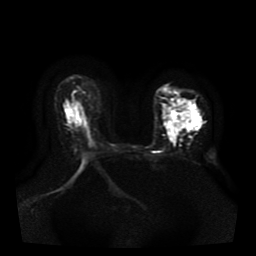
Breast MRI, one axial slice; position 27 of 41 along the scan axis; diffusion-weighted series; image 2 of 4 stored at this slice position (different b-values; order by instance number); 1.5 T; 256 × 256 image matrix, field of view 330 × 330 mm. Female patient.
Structures marked on this image (manually delineated by an expert):
- tumour on diffusion-weighted imaging: bounding box <164,99,198,140> (left, top, right, bottom; pixels)